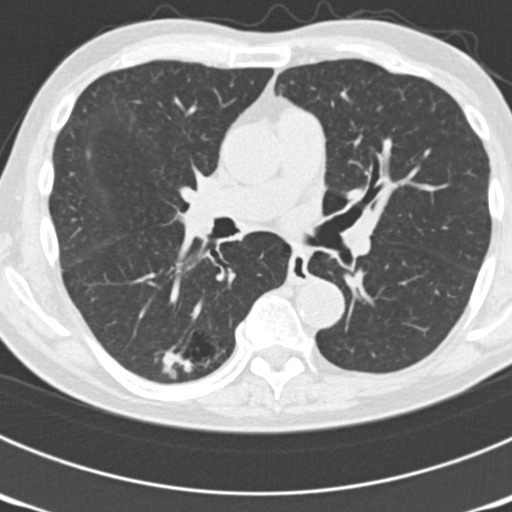
Low-dose screening chest CT, one axial slice. Slice 104 of 177 in the series (ordered by position). Reconstruction kernel B30f. 120 kVp. Lung window (W 1500 / L -600 HU). 2 mm slice thickness. 512 × 512 image matrix.
Structures marked on this image (outlined manually by an expert reader):
- lesion 5 (nodule, lower lobe of right lung): bounding box <163,352,192,376> (left, top, right, bottom; pixels)